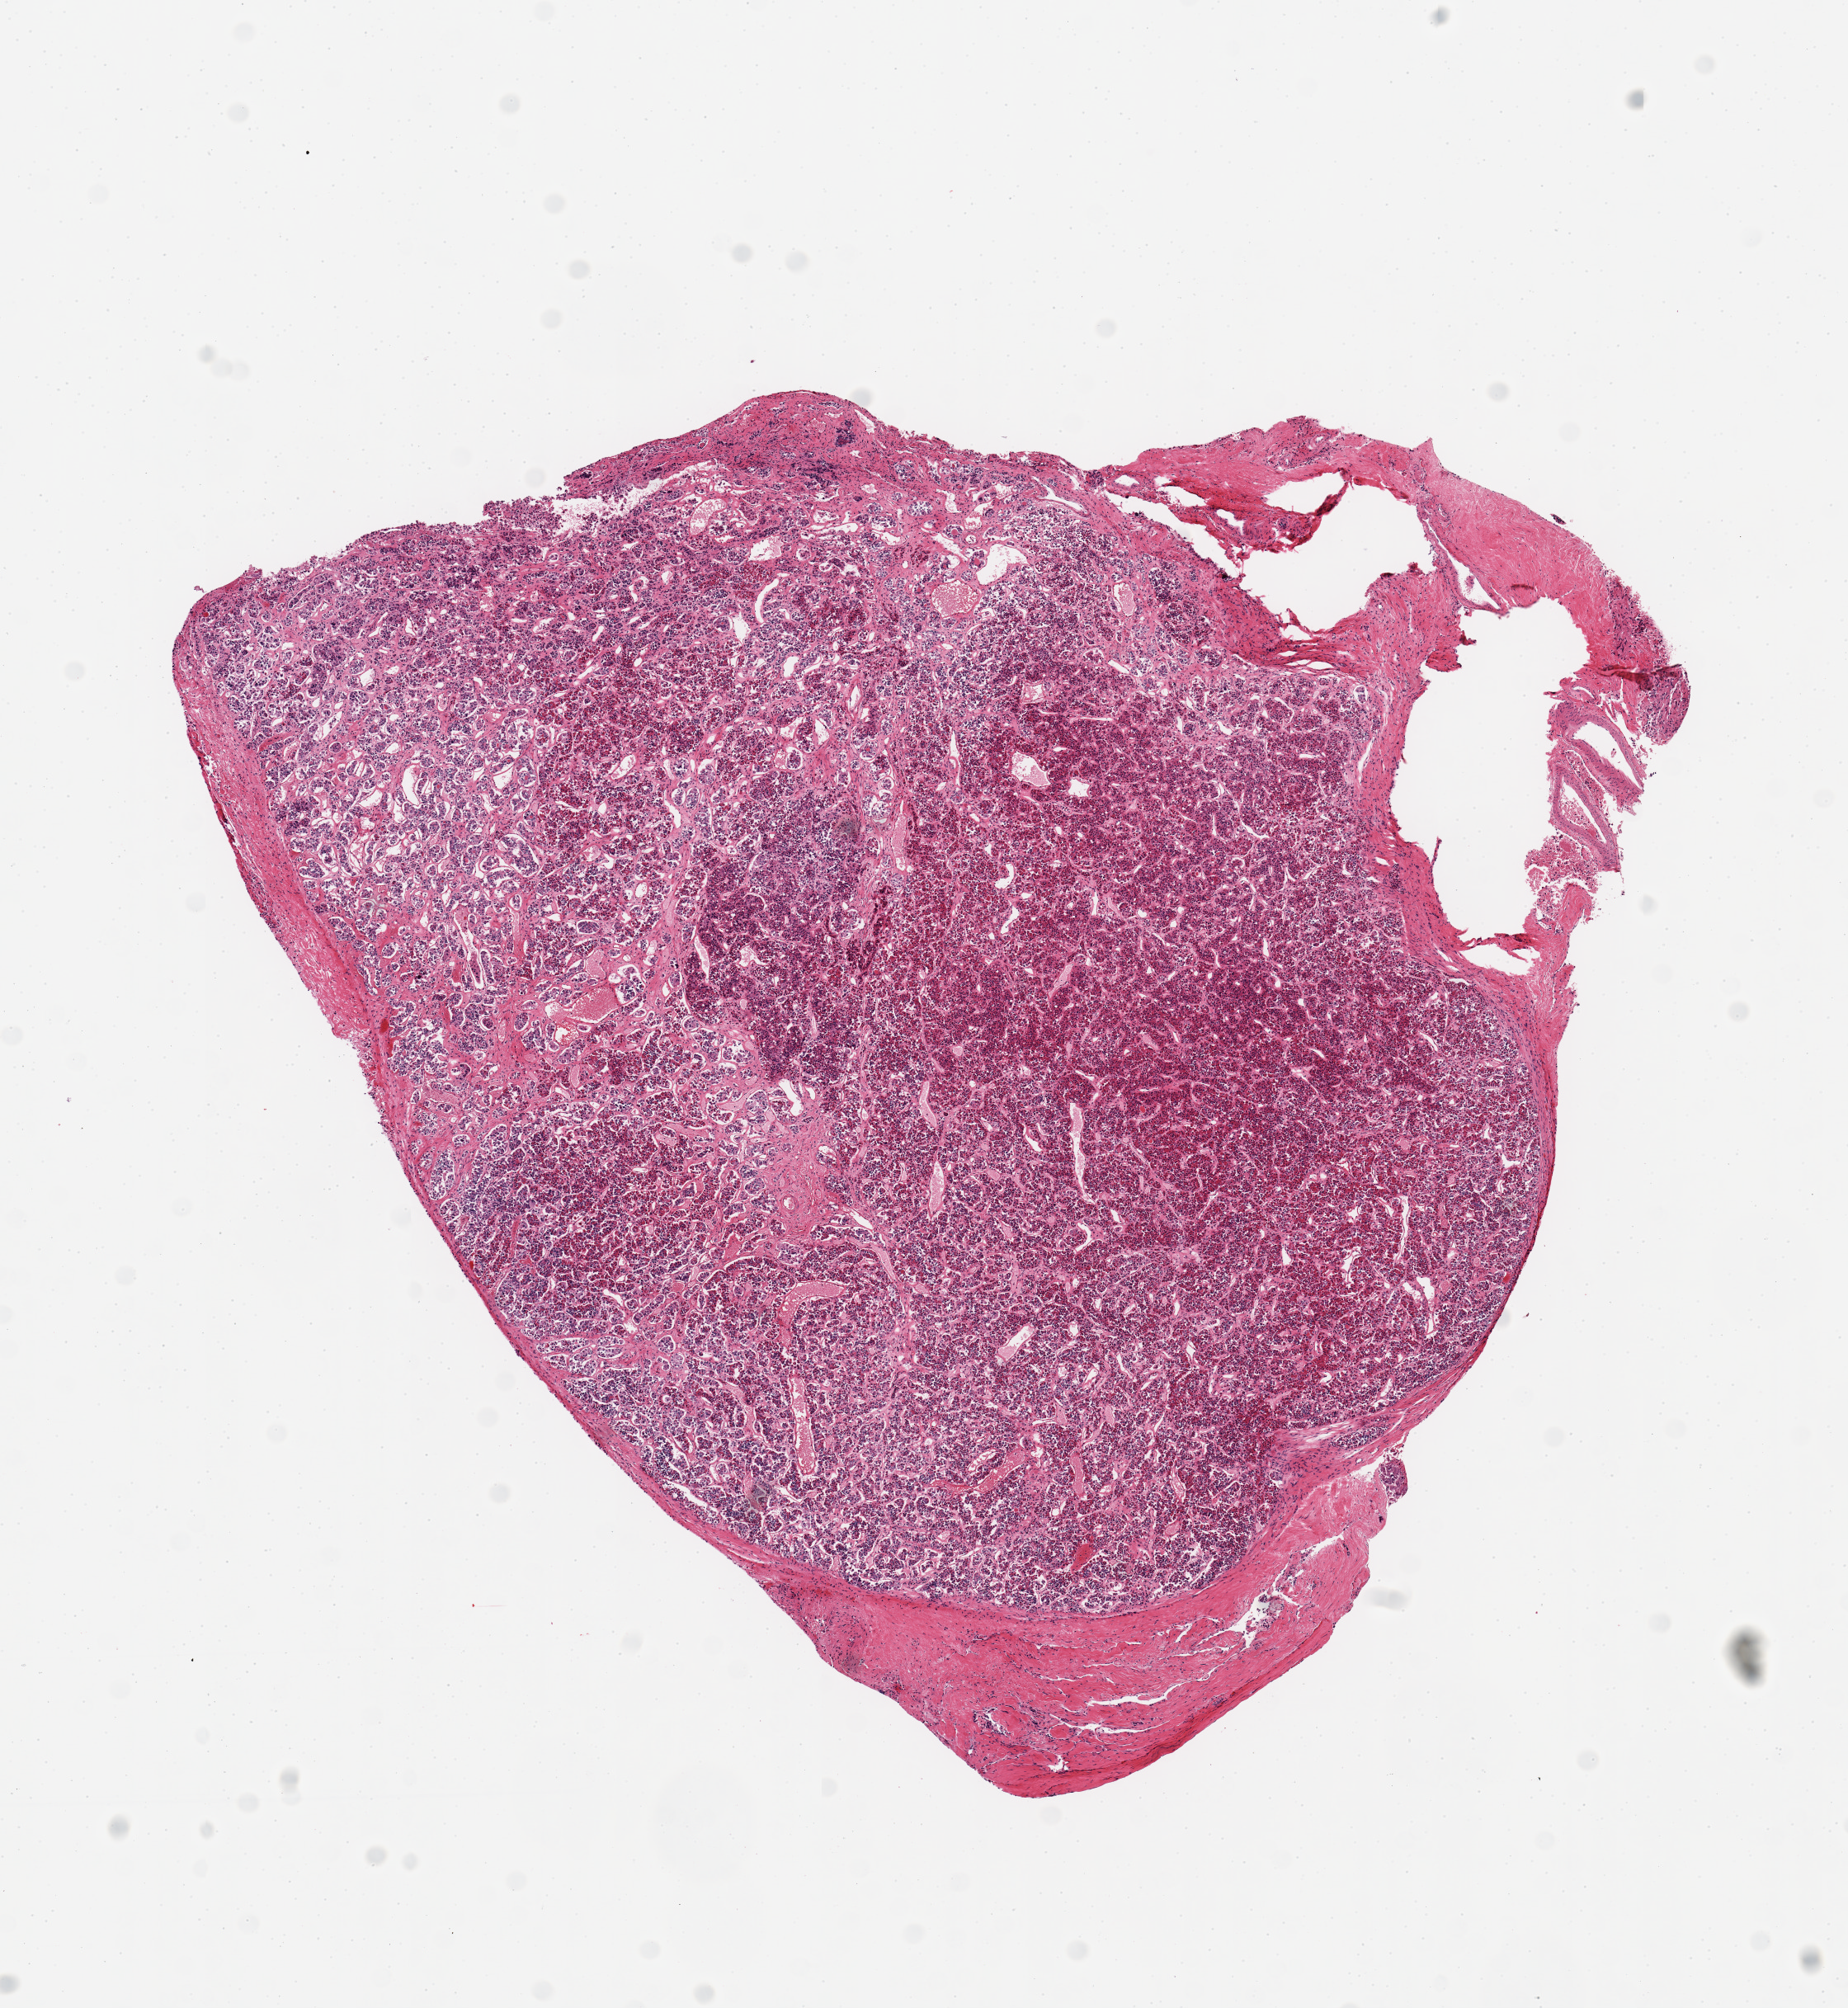
Digitized haematoxylin and eosin-stained section — whole scanned area (about 8.9 x 9.6 mm) shown as a low-resolution overview; PAXgene-fixed, paraffin-embedded tissue; section of pituitary (target tissue); donor tissue sample. Donor: male.
* reviewer comment on this tissue sample: 1 piece; all adenohypophysis; no neural elements in this cut